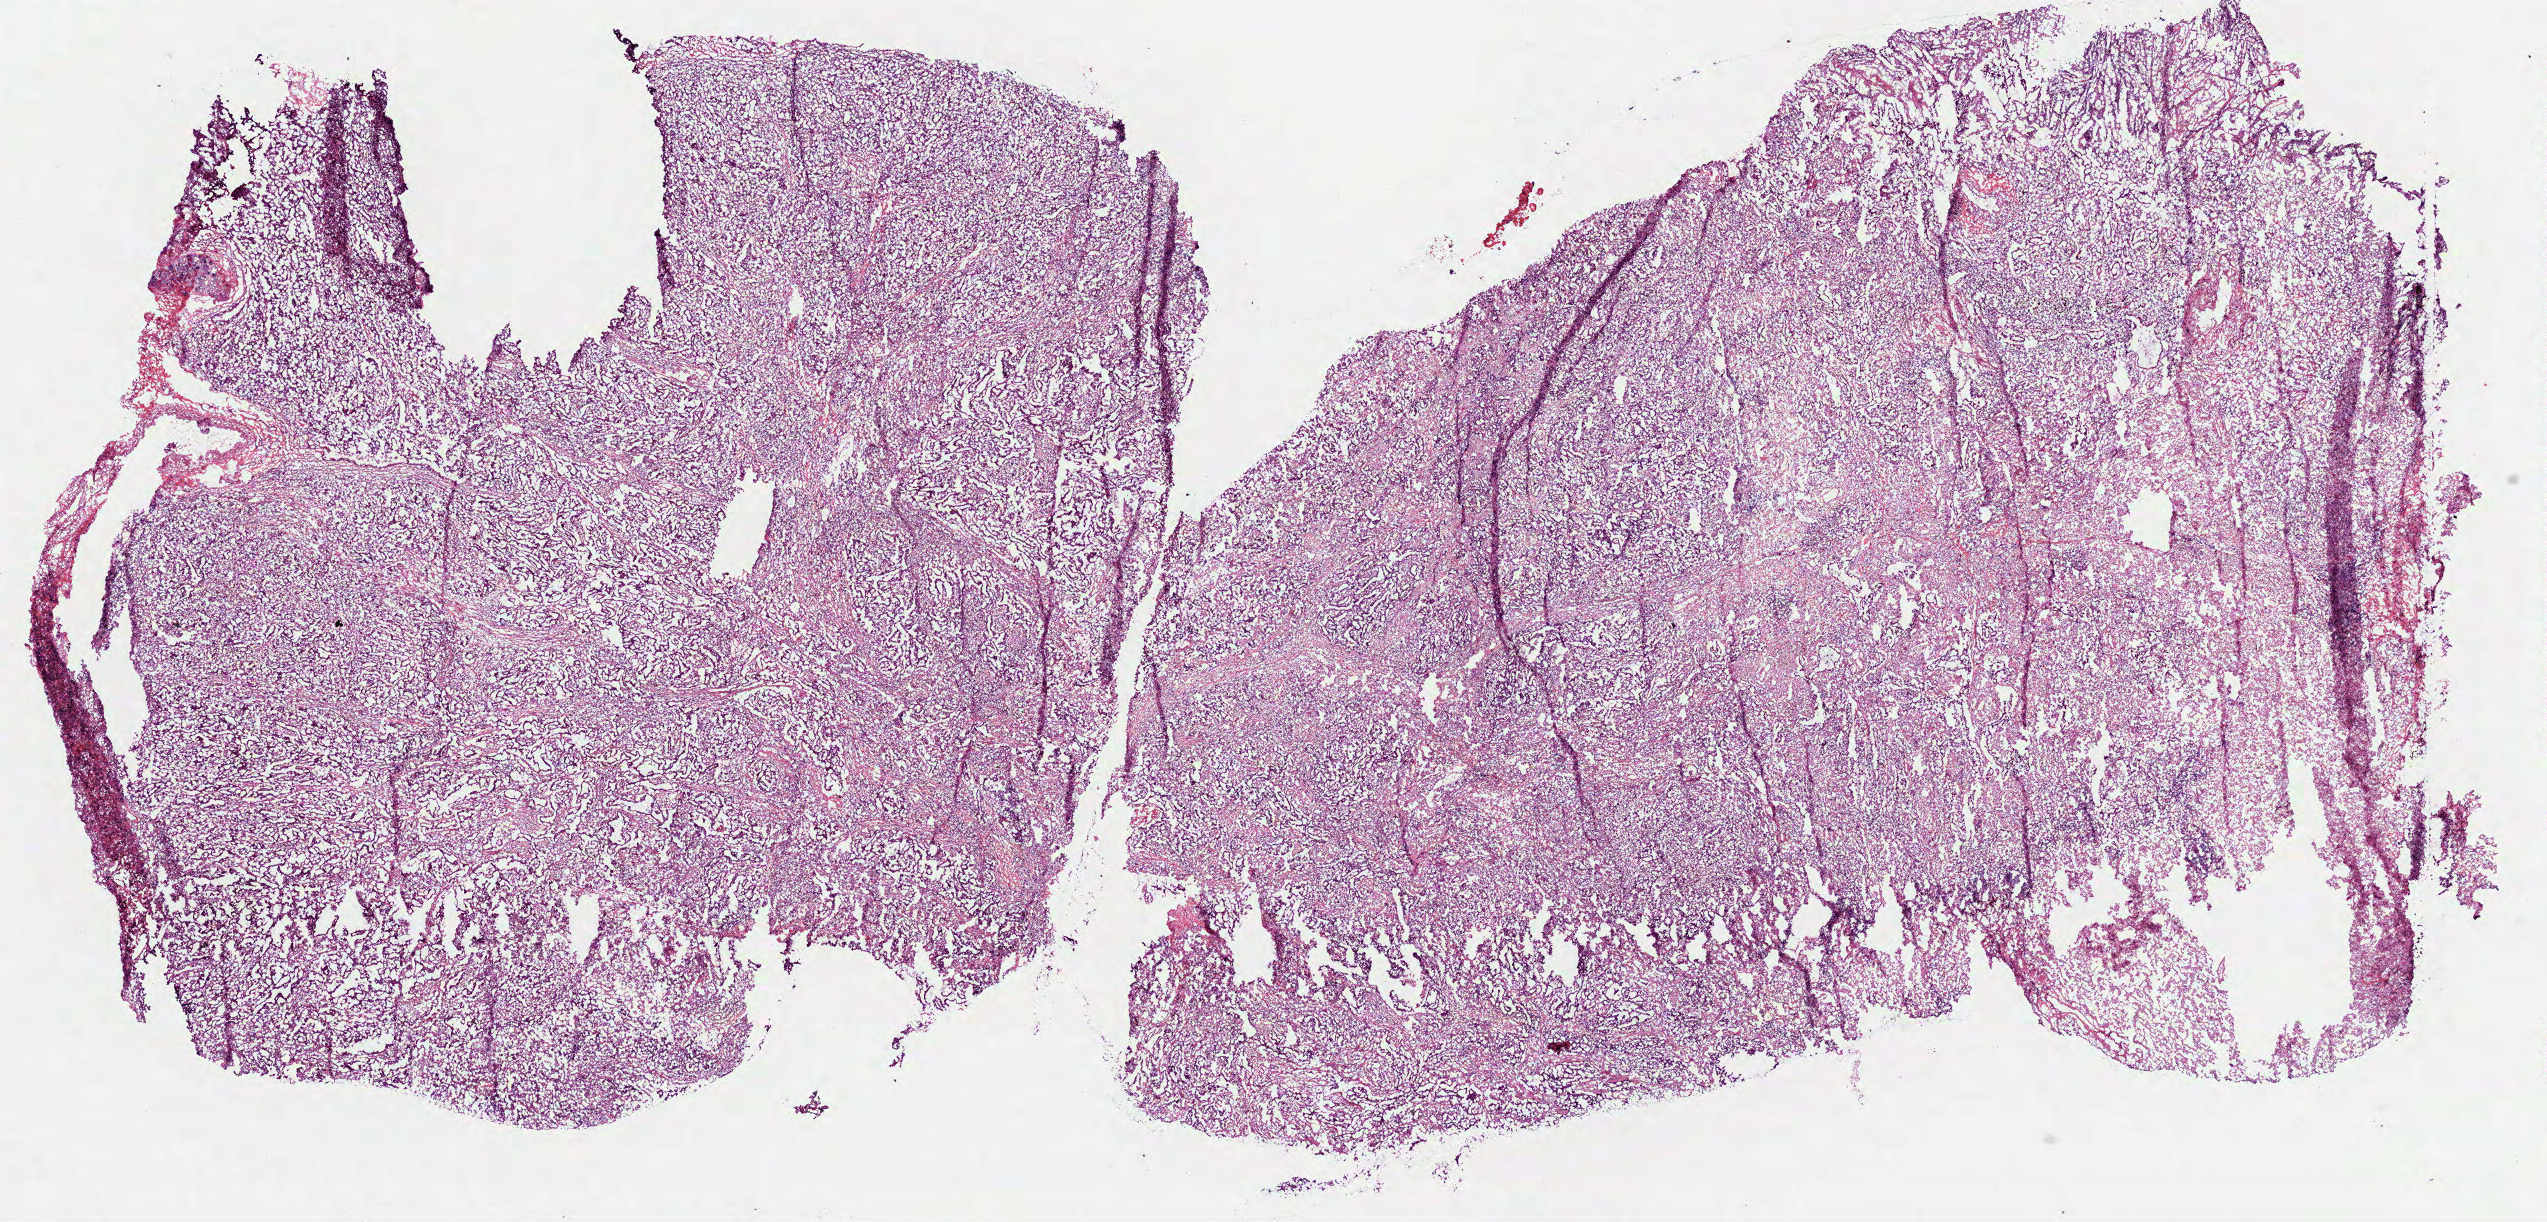
Whole-slide histology image, H&E — whole scanned area (about 20.5 x 9.9 mm) shown as a low-resolution overview. Frozen section from the bottom of the tissue portion. Primary tumour sample from the lung. Patient: female, age at initial diagnosis 81 years. Composition of this section per pathologist review: tumour cells 80%, tumour nuclei 55%, normal cells 0%, stromal cells 20%, necrosis 0%. Inflammatory infiltration, as recorded: lymphocyte infiltration 20%, monocyte infiltration 5%, neutrophil infiltration 5%.
AJCC pathologic stage: IB (7th edition). Pathologic diagnosis: Adenocarcinoma with mixed subtypes (upper lobe, lung).